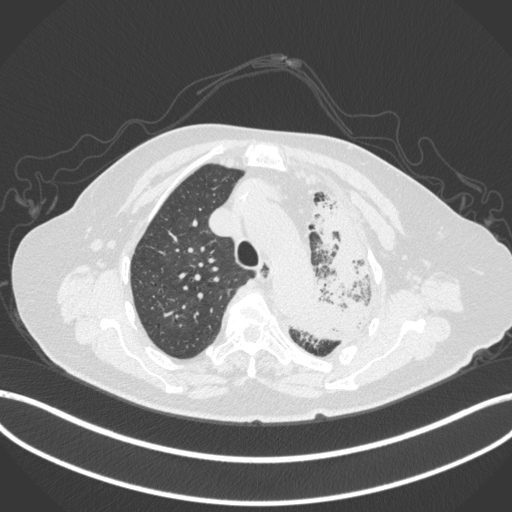
Chest CT, one axial slice; reconstruction kernel B31f; 120 kVp; lung window (W 1500 / L -600 HU); 1 mm slice thickness; 512 × 512 image matrix. Female patient, age 75 years. From the clinical record (not read from this slice): clinical TNM (as recorded): T3 N3 M1.
Outlined on this slice (rectangle marked by the reading radiologist):
- lung tumour (recorded histology: adenocarcinoma): bounding box <285,195,383,344> (left, top, right, bottom; pixels)